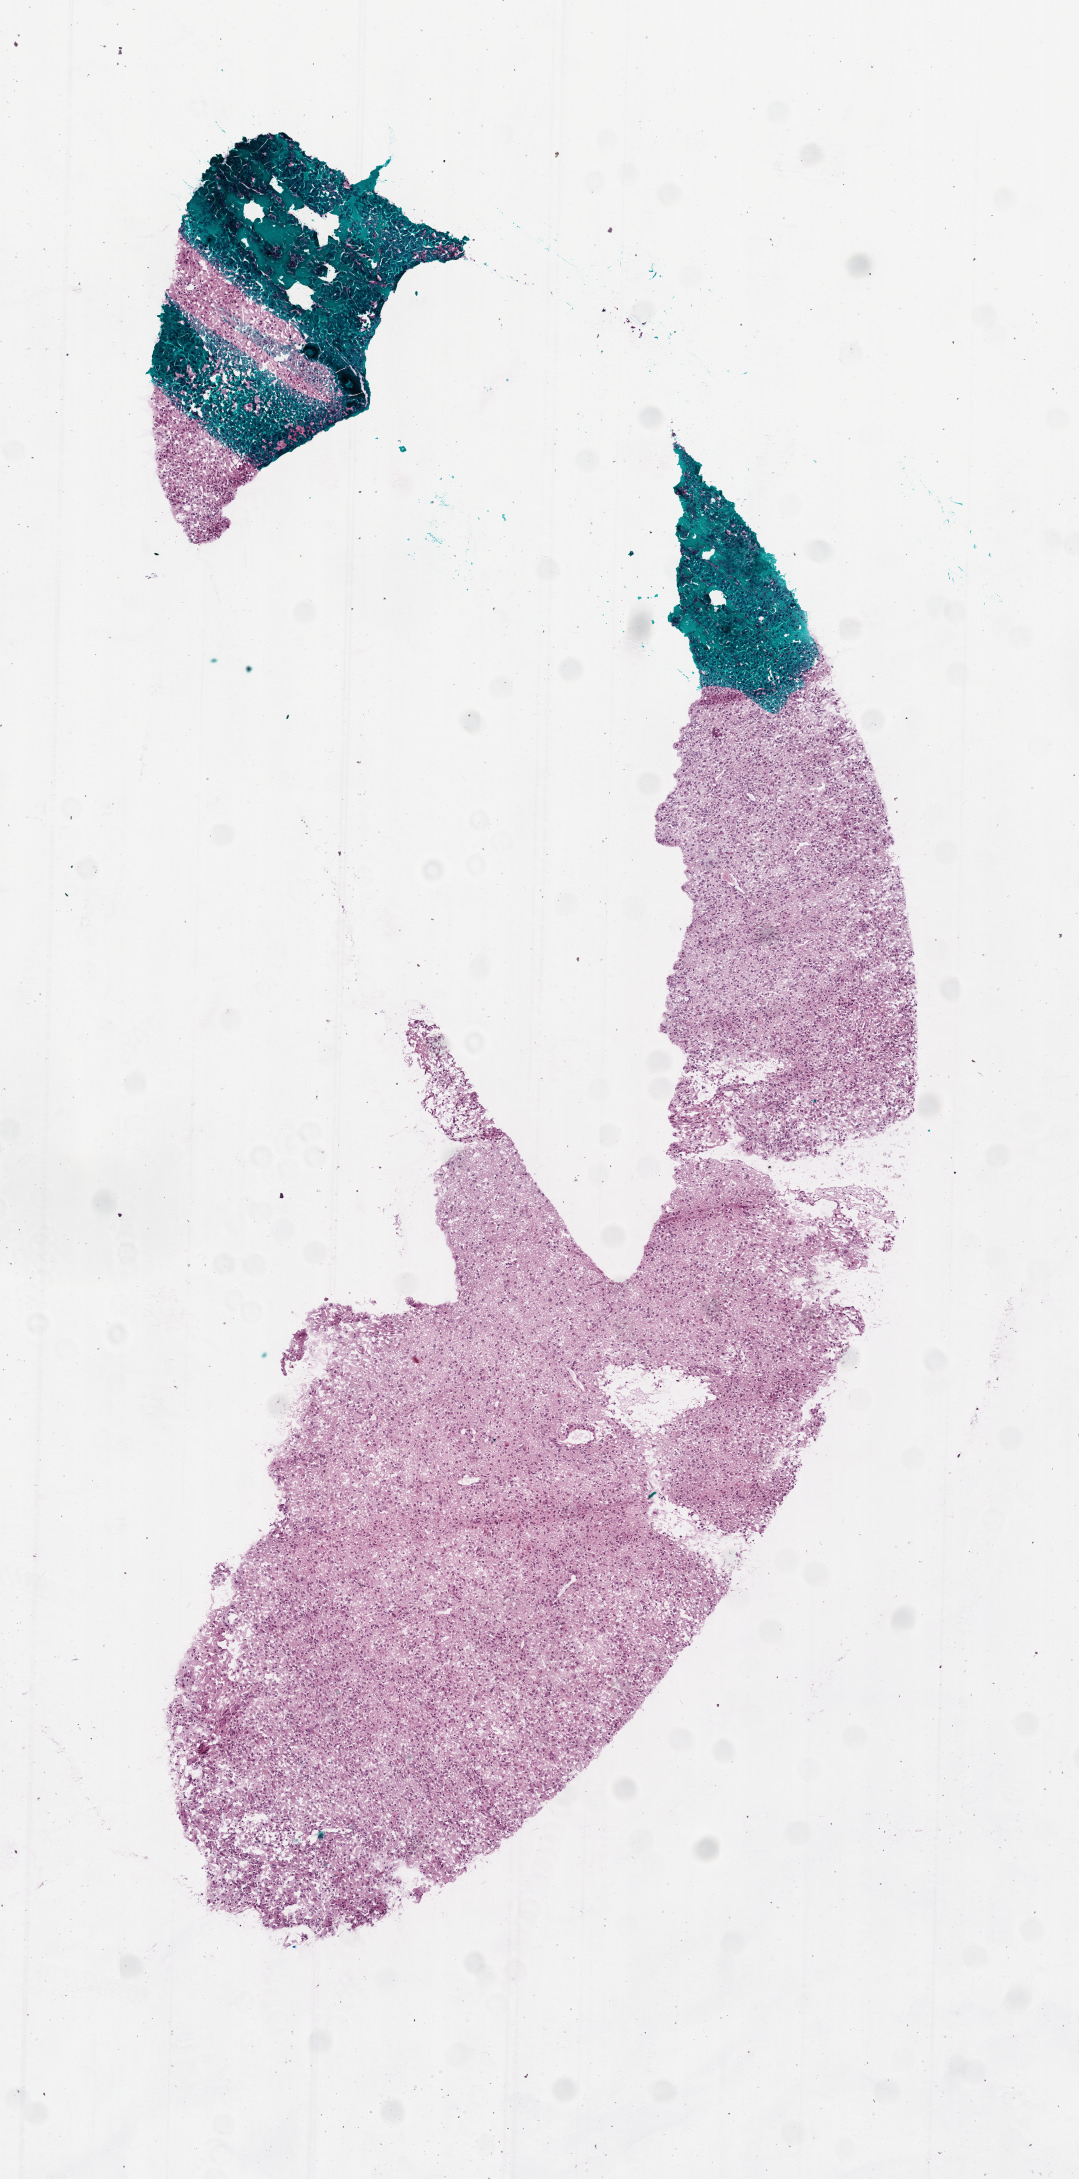
Digitized H&E tissue section (whole slide) — shown as a low-resolution overview of the whole scanned area (about 4.4 x 8.8 mm), frozen section, primary tumour sample from the brain. Patient: male, age at initial diagnosis 63 years. Pathologist review of this section (percent, as recorded): tumour cells 75%, tumour nuclei 95%, normal cells 0%, stromal cells 20%, necrosis 5%.
Pathologic diagnosis: Glioblastoma.